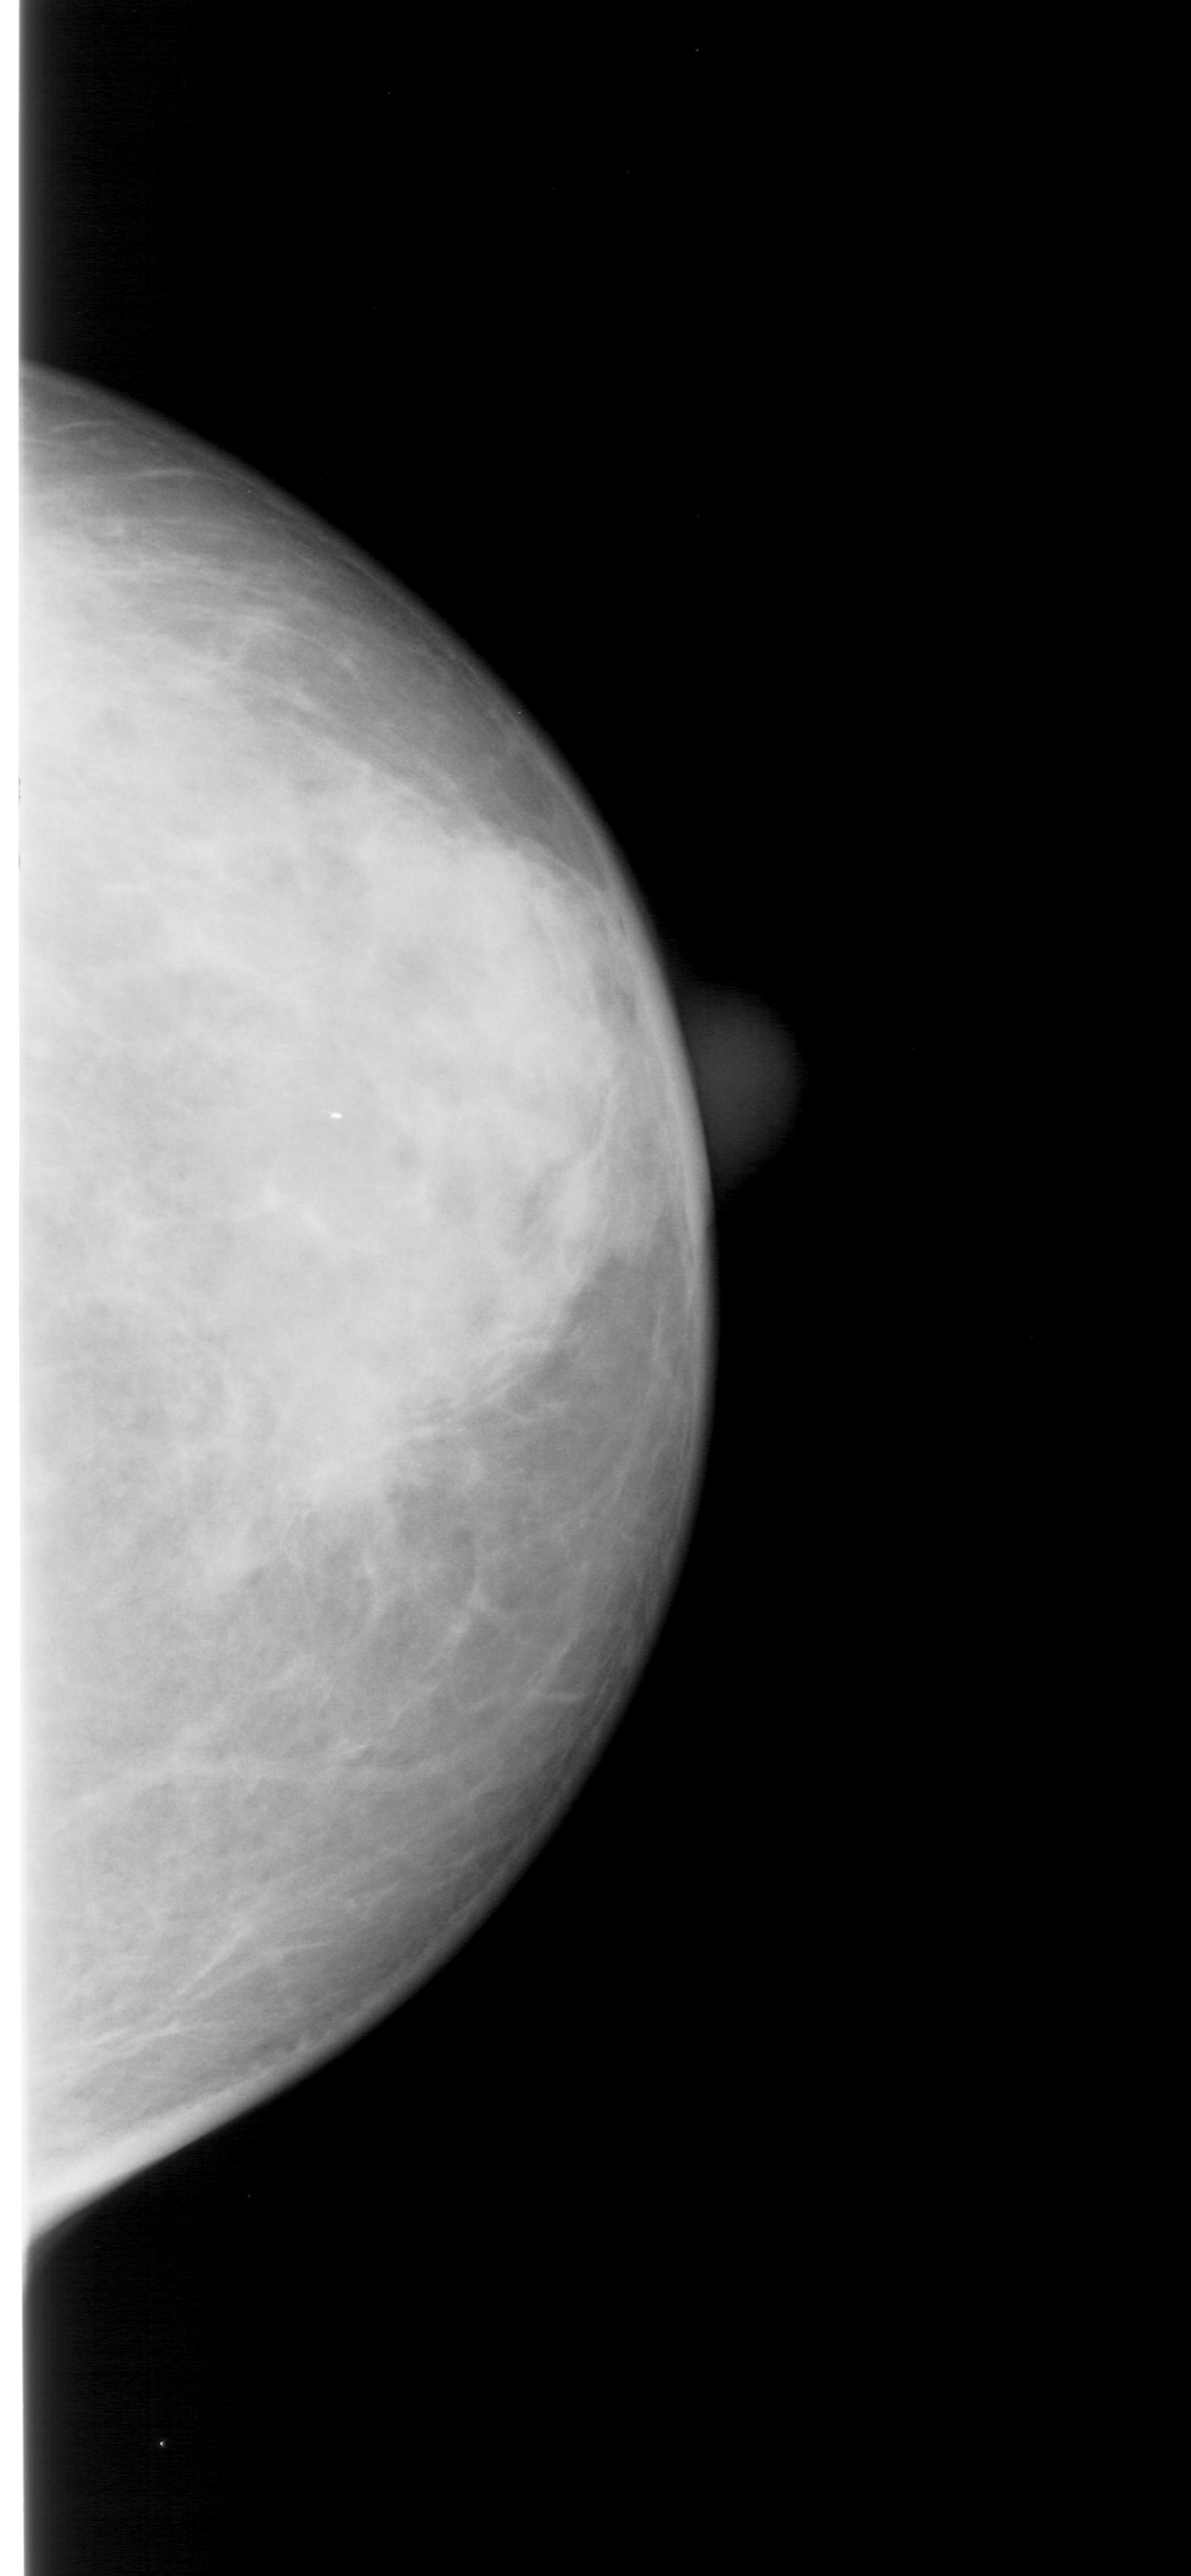
Digitized screen-film mammogram, right breast, craniocaudal (CC) view, BI-RADS breast density category 4 (scale 1–4).
Calcifications, morphology pleomorphic, distribution clustered; BI-RADS assessment category 5; subtlety rating 3 on a 1 (subtle) to 5 (obvious) scale; pathology result (as recorded, not read from the image): malignant.